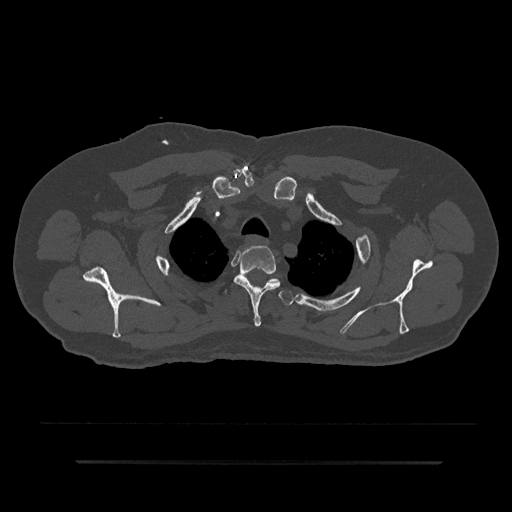
CT including the spine, one axial slice. Position 690 of 797 along the scan axis. Reconstruction kernel Br40s/3. Bone window (W 1800 / L 400 HU). 0.5 mm slice thickness. 512 × 512 image matrix. Patient: male, 59 years. From the clinical record (not read from this slice): primary cancer: bile ducts; vertebrae with lytic lesions (as recorded): T10.
Outlined on this slice (semi-automatically segmented with operator editing):
- T2 vertebra: box from (x=234, y=246) to (x=281, y=327) px
- T3 vertebra: (x=225, y=290)–(x=293, y=306)